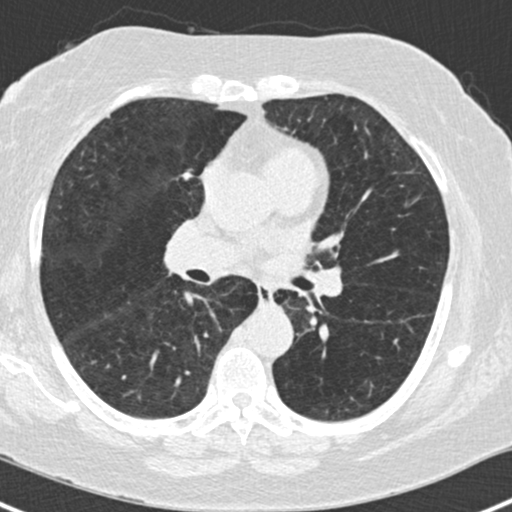
Low-dose screening chest CT, one axial slice; position 83 of 168 along the scan axis; 120 kVp; lung window (W 1500 / L -600 HU); 2 mm slice thickness; 512 × 512 image matrix, field of view 303 × 303 mm.
Structures marked on this image (outlined manually by an expert reader):
- lesion 1 (tumor, upper lobe of right lung): bounding box [x1, y1, x2, y2] px = [180, 170, 193, 180]